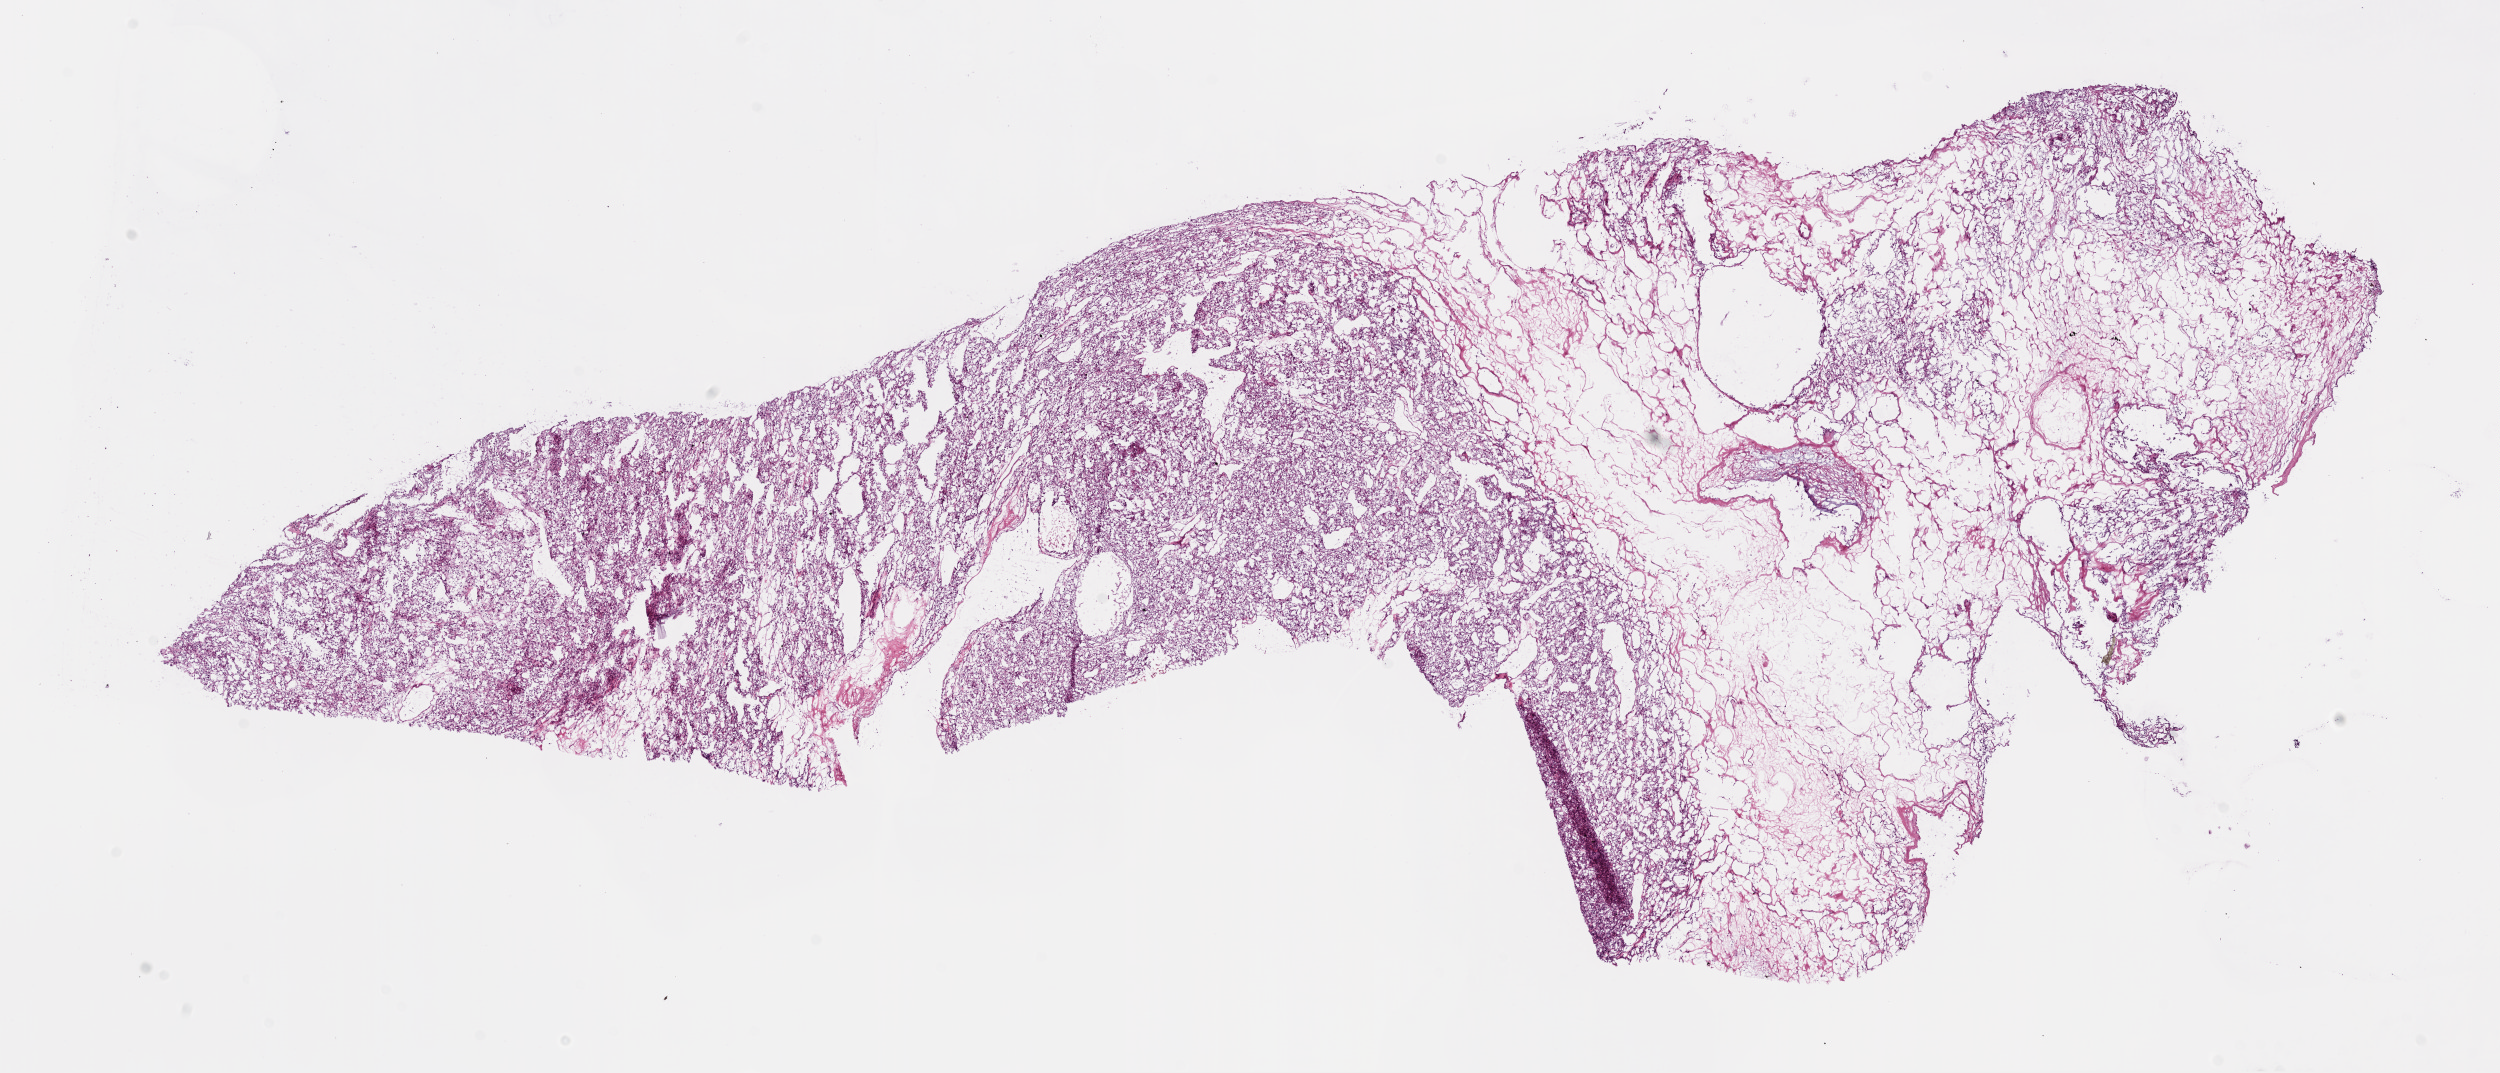
H&E whole-slide image — low-resolution overview of the scanned area, about 20.1 x 8.6 mm (from a 20x scan). Frozen section from the bottom of the tissue portion. Primary tumour sample from the kidney. Female, age 75 years at initial diagnosis. Histologic grade: G3 (poorly differentiated). Slide review estimates, as recorded: tumour cells 60%, tumour nuclei 85%, normal cells 0%, stromal cells 40%, necrosis 0%.
Histologic diagnosis: Clear cell adenocarcinoma, NOS. Laterality: left. AJCC pathologic stage: III.